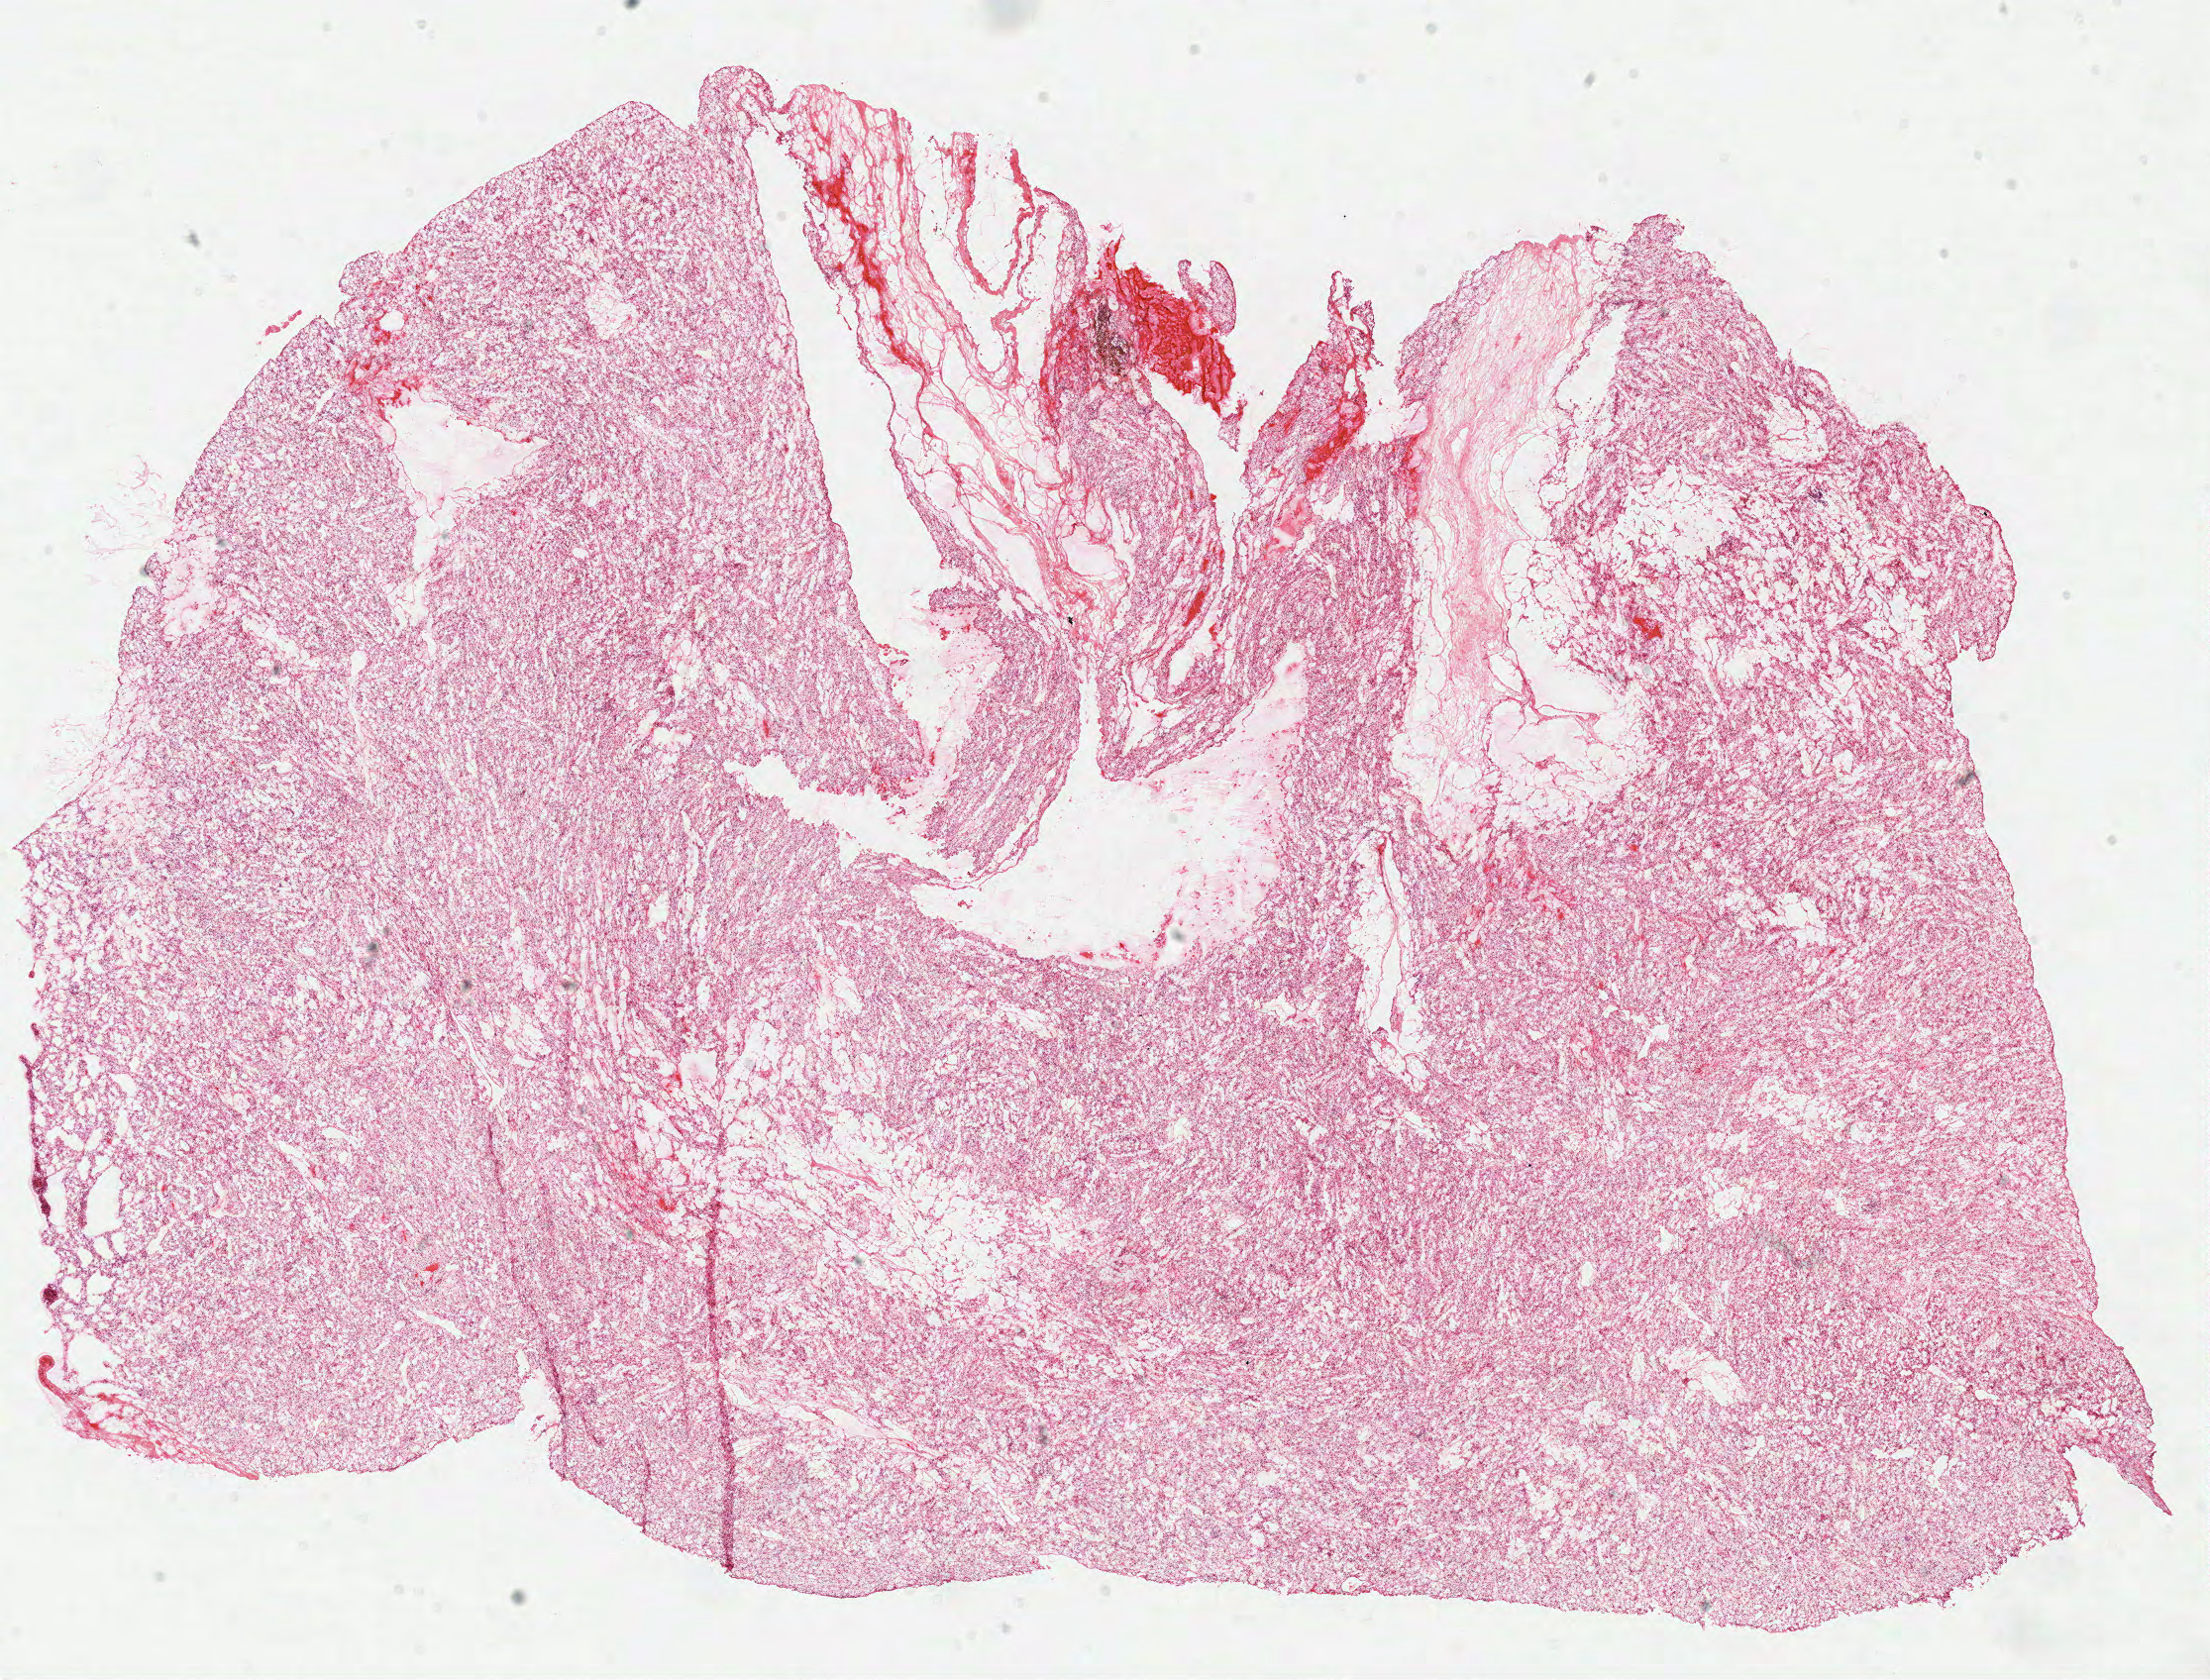
Digitized Hematoxylin and eosin (H&E) stained tissue section (whole slide), a low-resolution overview of the entire scanned area, about 17.6 x 13.4 mm (slide scanned at 40x); frozen section from the top of the tissue portion; sample: primary tumour, kidney. Male, age 60 years at initial diagnosis. Histologic grade: G2 (moderately differentiated). Composition of this section per pathologist review: tumour cells 90%, tumour nuclei 85%, normal cells 0%, stromal cells 10%, necrosis 0%.
Lymph nodes positive (case pathology): 0 of 1 examined. Histologic diagnosis: Clear cell adenocarcinoma, NOS. AJCC pathologic stage: II (6th edition).